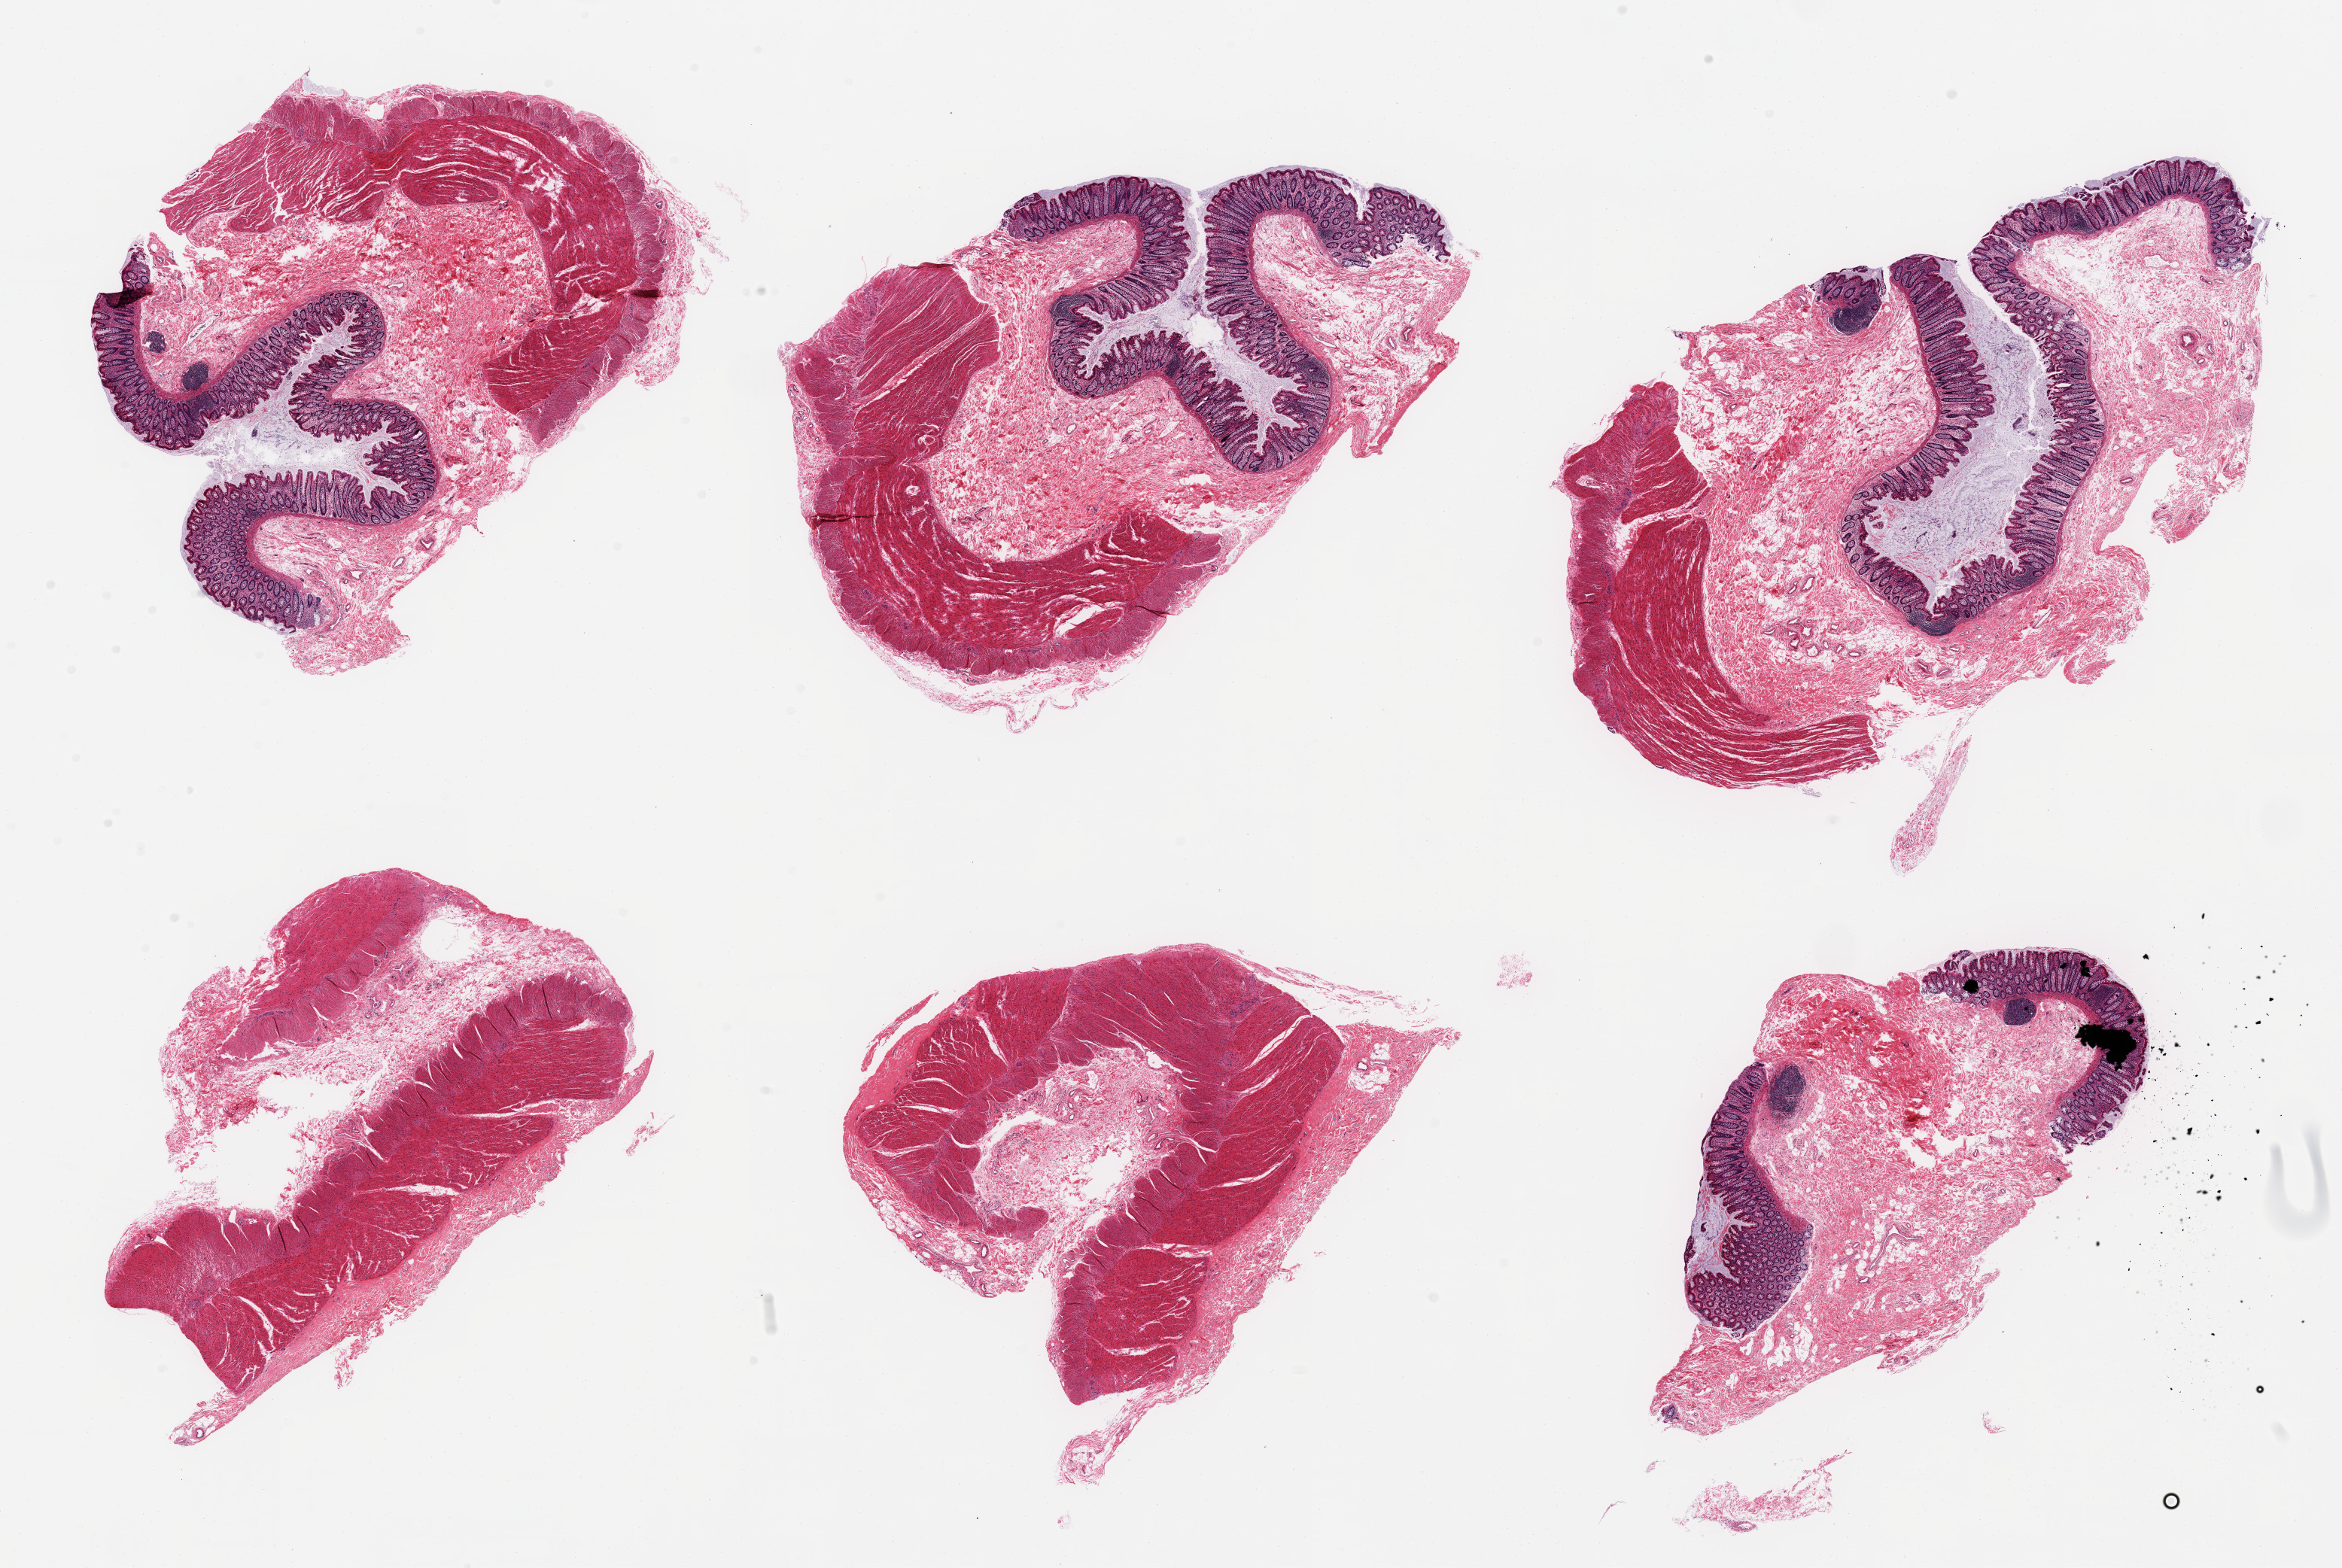
Digitized hematoxylin and eosin (H&E)-stained section, a low-resolution overview of the entire scanned area, about 24.6 x 16.5 mm (slide scanned at 20x), PAXgene-fixed, paraffin-embedded tissue, target tissue: transverse colon, donor tissue sample. Donor: female.
Pathologist's review note for this sample: 6 pieces, target mucosa well preserved, up to ~0.5mm, ~10% of thickness in 4/6 sections.